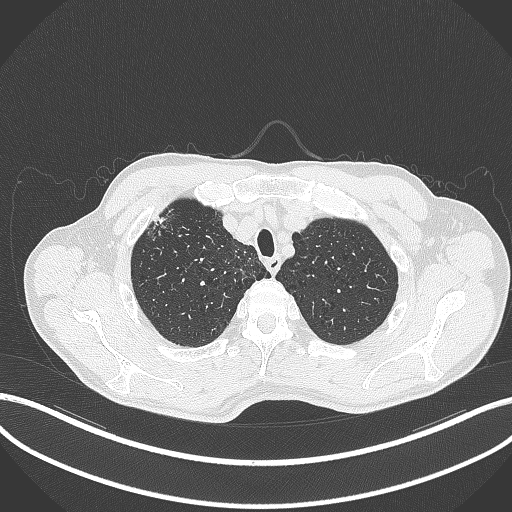
Chest CT, one axial slice. Position 363 of 427 along the scan axis. 120 kVp. Lung window (W 1500 / L -600 HU). 1 mm slice thickness. 512 × 512 image matrix, field of view 400 × 400 mm. Male patient, age 69 years. Case-level facts recorded for this patient, not image findings: clinical TNM (as recorded): T1b N1 M0.
Annotated regions visible in this slice (bounding box drawn by a radiologist):
- lung tumour (recorded histology: adenocarcinoma): bounding box [x1, y1, x2, y2] px = [150, 211, 172, 232]